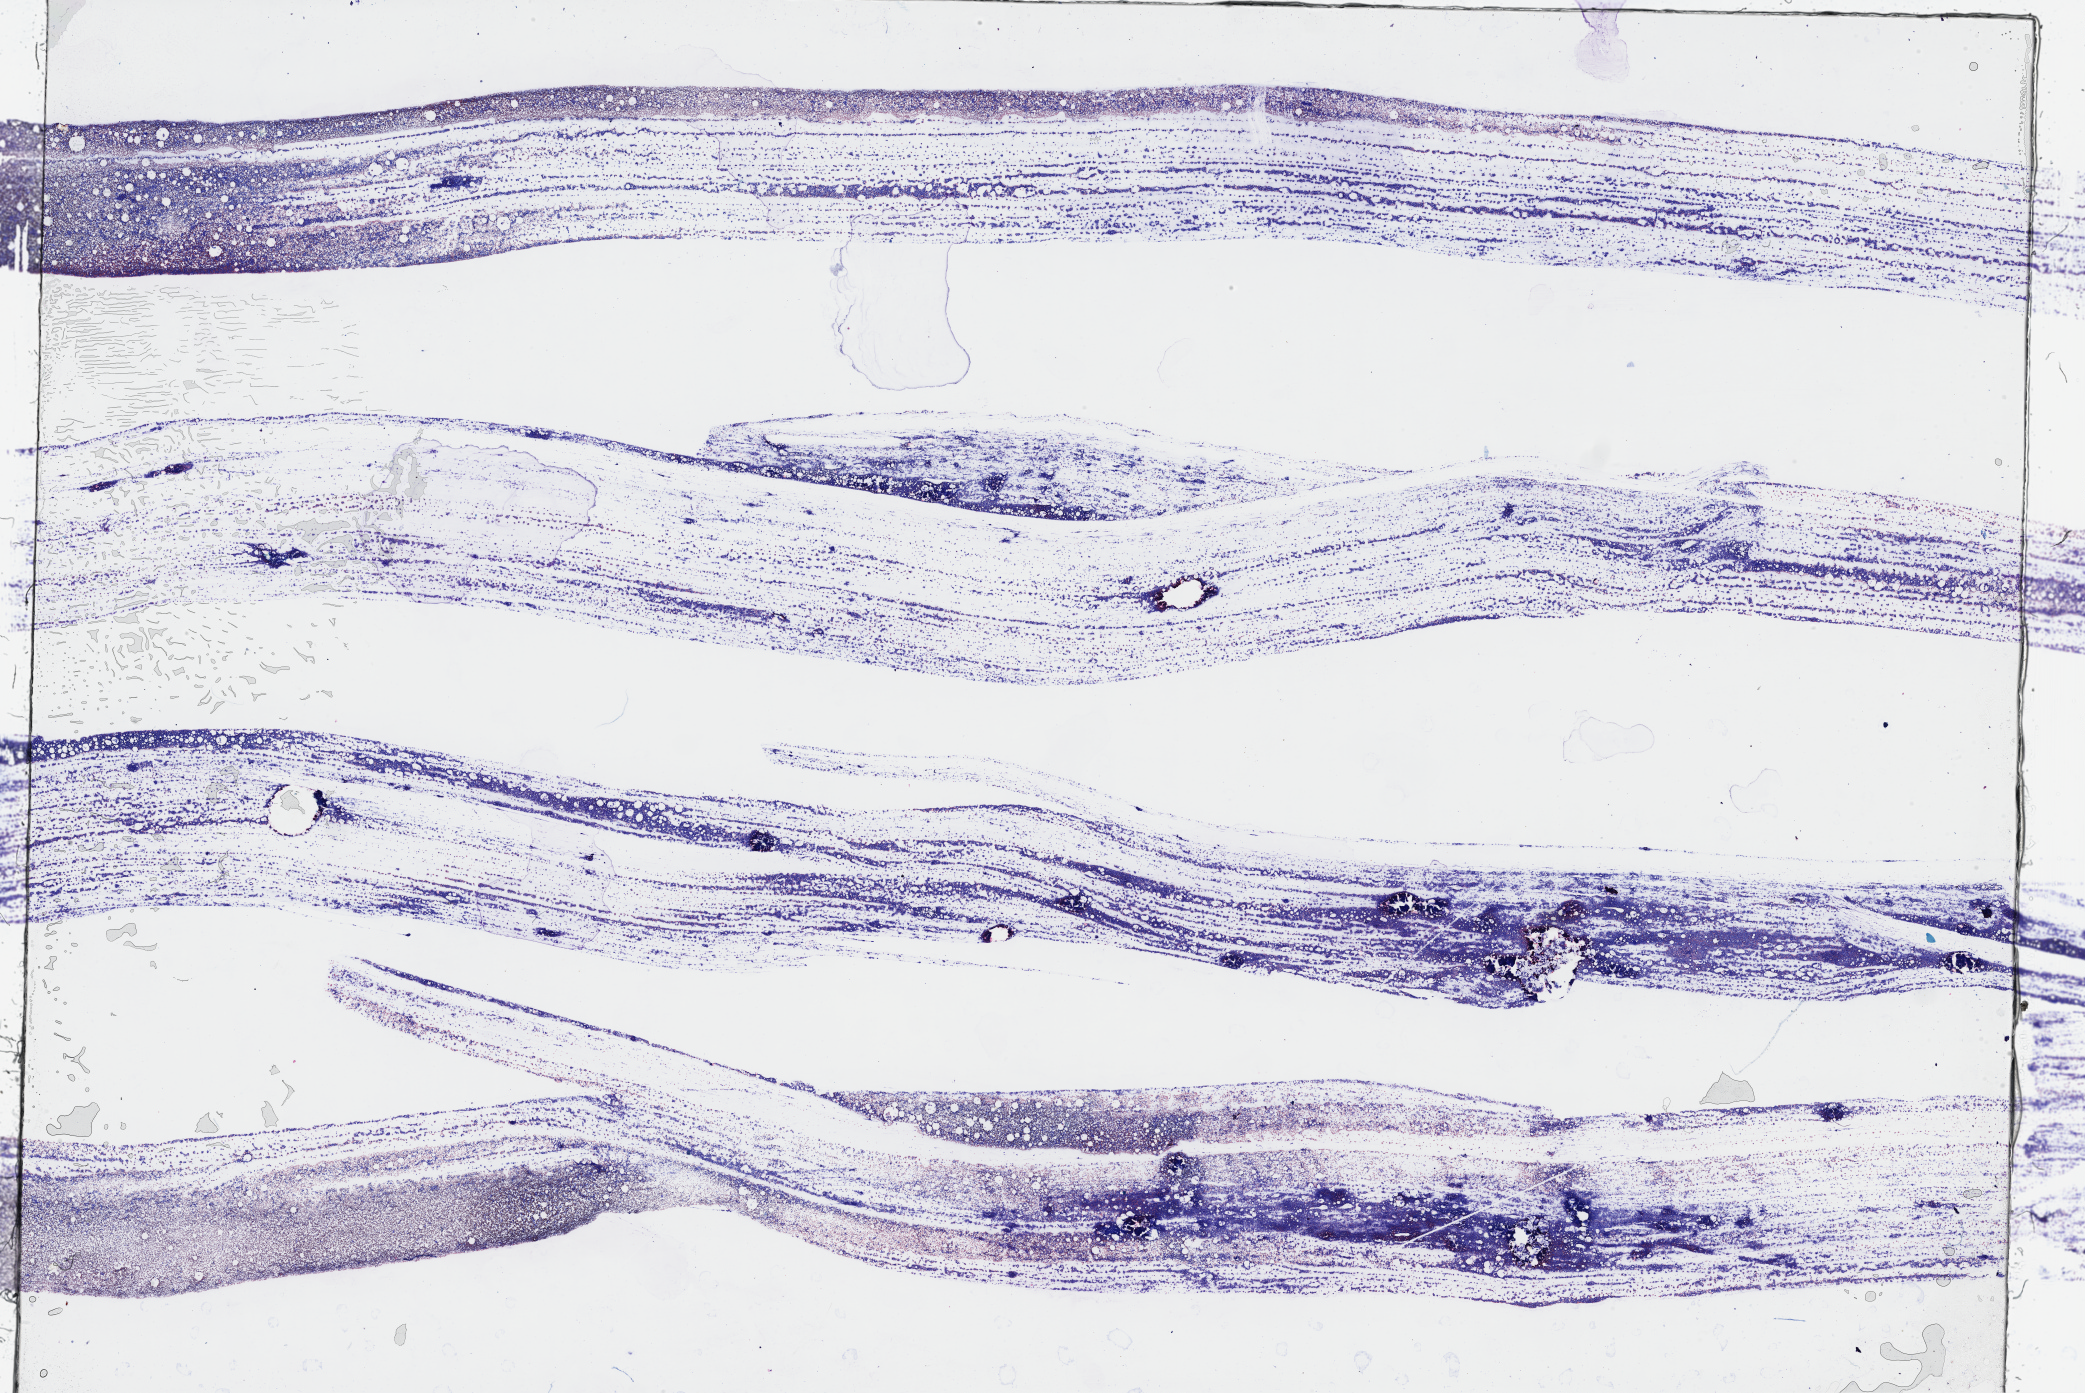
Whole-slide histology image, H&E-stained — a low-resolution overview of the entire scanned area, about 33.7 x 22.5 mm (slide scanned at 40x), bone marrow (leukaemic) sample. 71-year-old female patient. Blasts: 40%.
FAB classification: M2. Diagnosis: Acute Myeloid Leukemia.